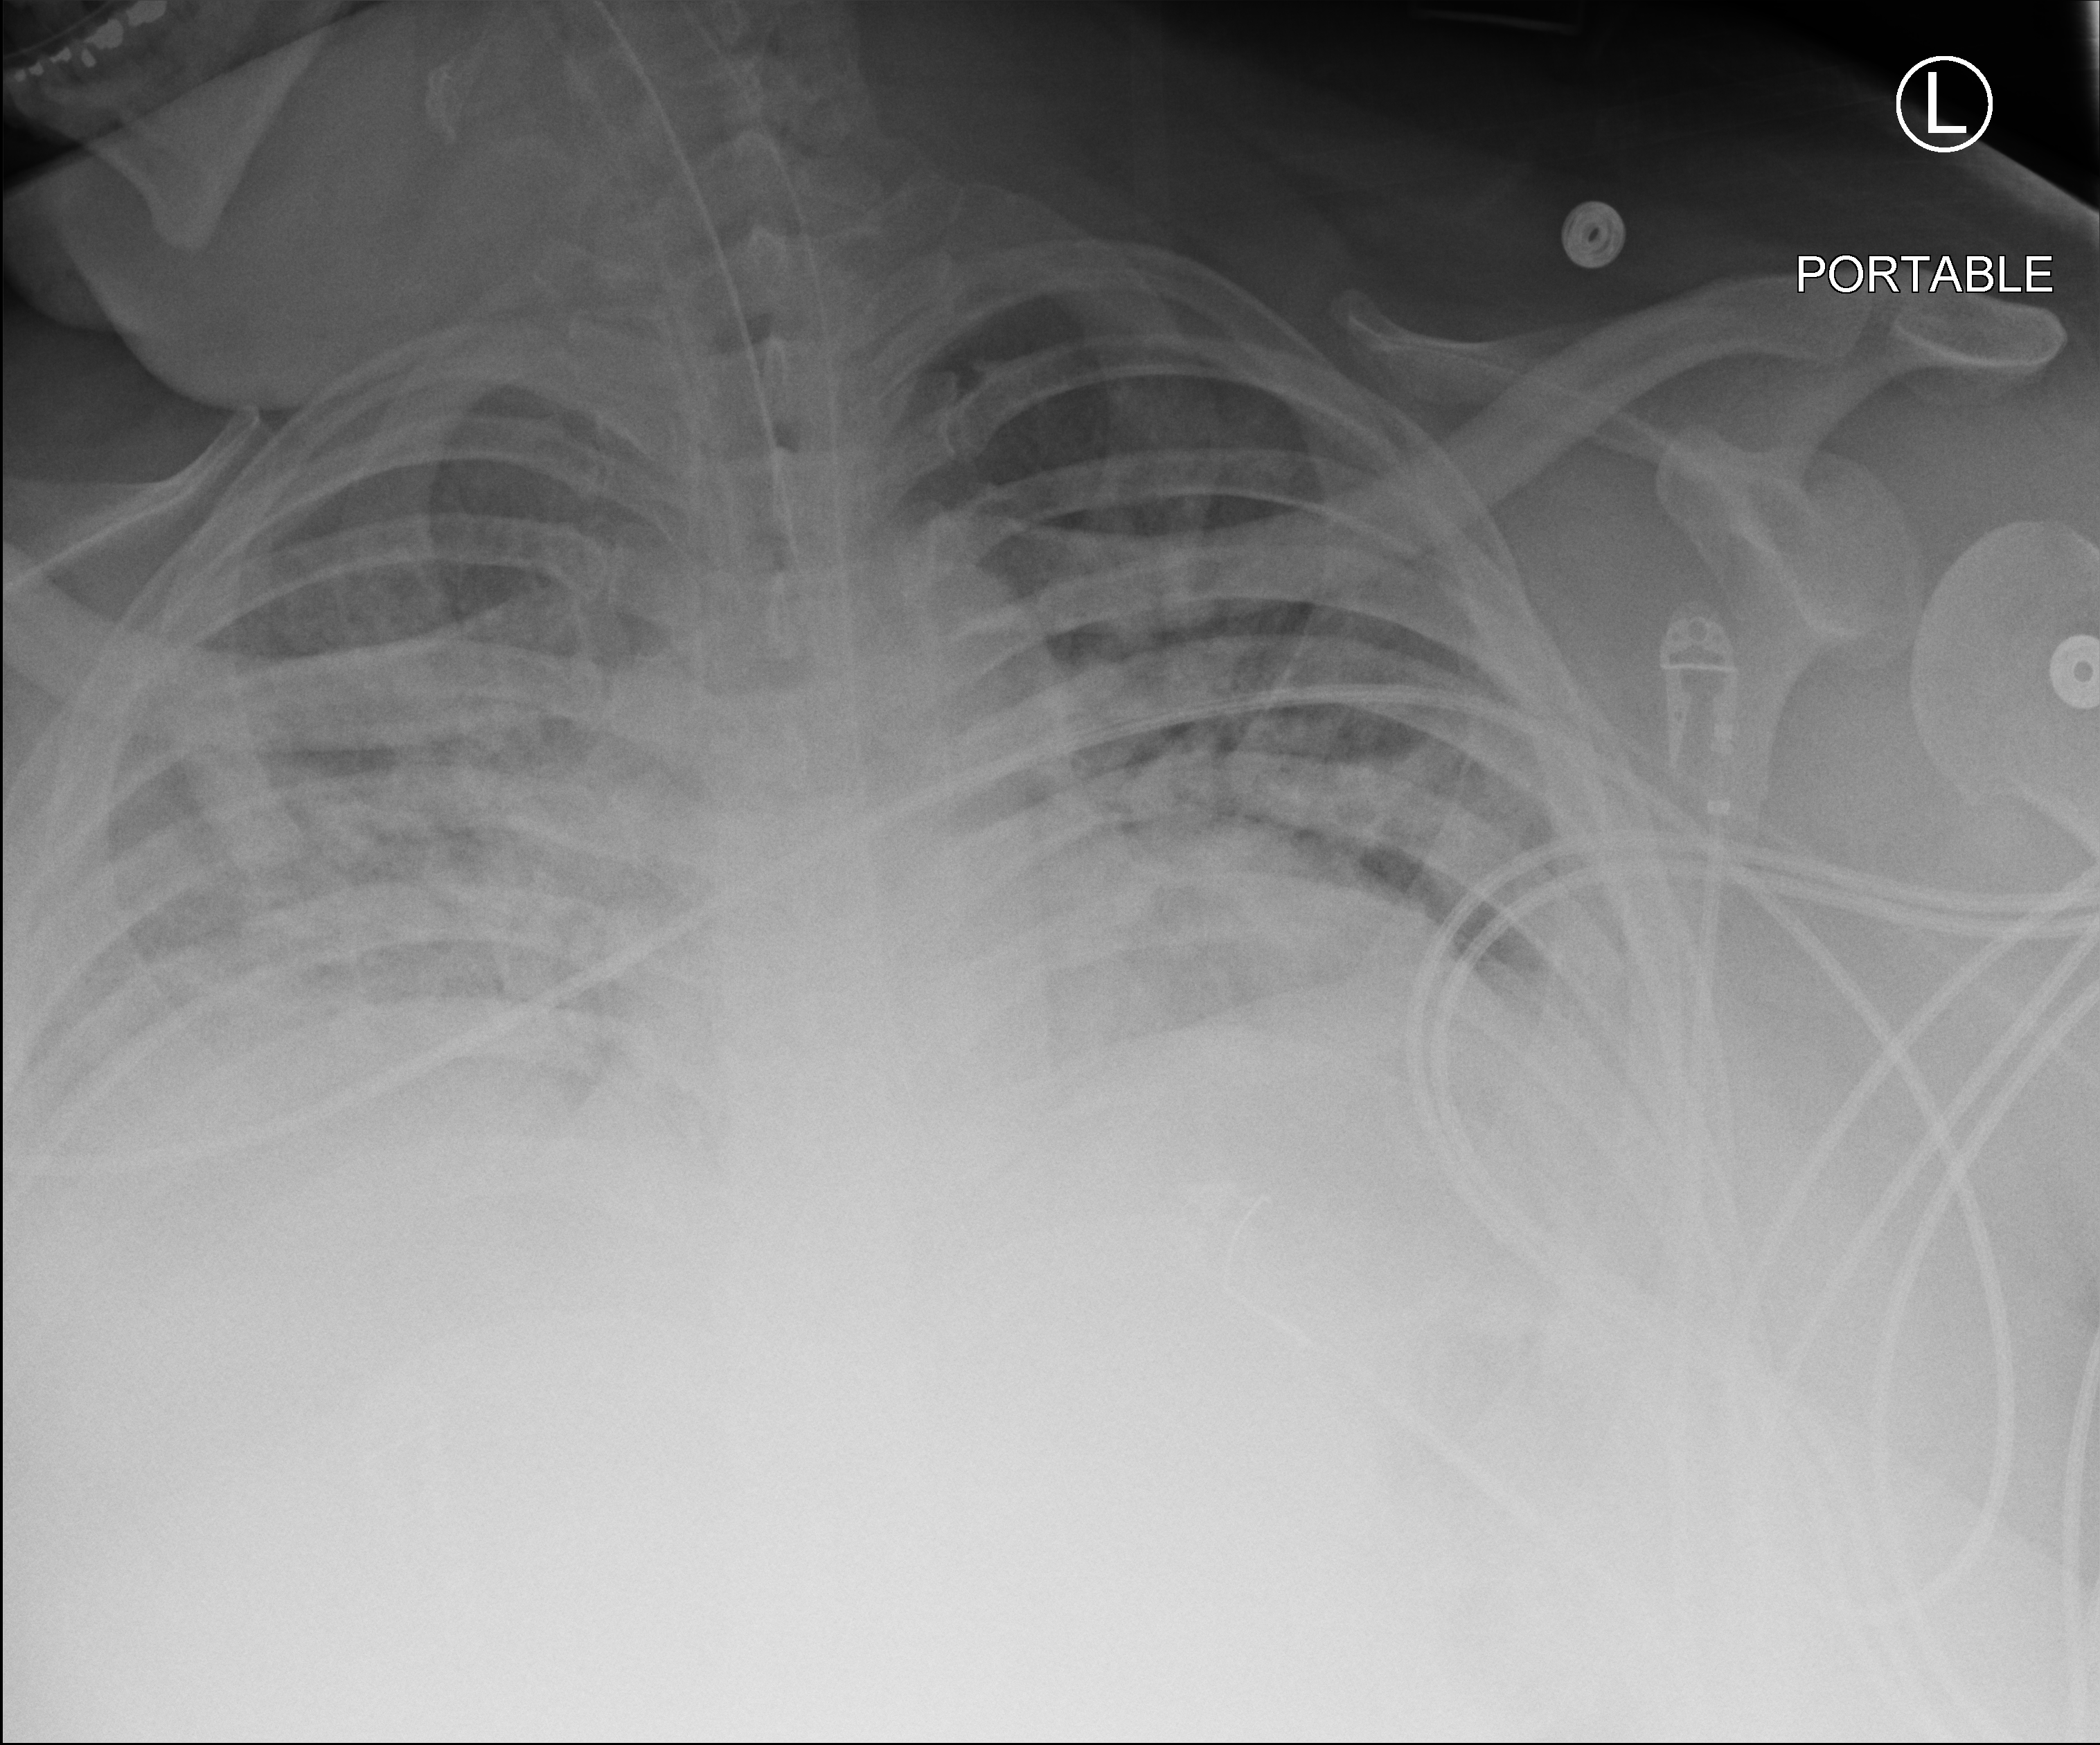
Chest X-ray (portable); anteroposterior (AP) projection. Male patient hospitalised with COVID-19, age 18–59 years.
Admission-level facts for this patient (not findings on this image; timing relative to this image not recorded): admitted to intensive care during this hospital stay: yes; length of hospital stay: 69 days.